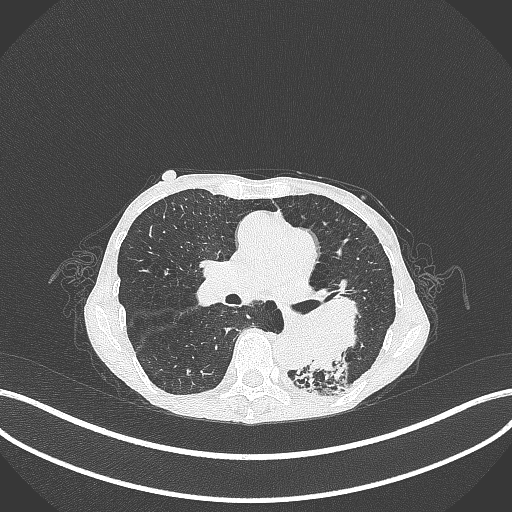
Chest CT, one axial slice. Position 150 of 347 along the scan axis. Lung window (W 1500 / L -600 HU). 512 × 512 image matrix, field of view 400 × 400 mm. Female patient, age 70 years. Case-level facts recorded for this patient, not image findings: clinical TNM (as recorded): T3 N0 M0; histopathological grade: G3.
Outlined on this slice (bounding box drawn by a radiologist):
- lung tumour (recorded histology: small cell carcinoma): bounding box [x1, y1, x2, y2] px = [272, 296, 373, 384]